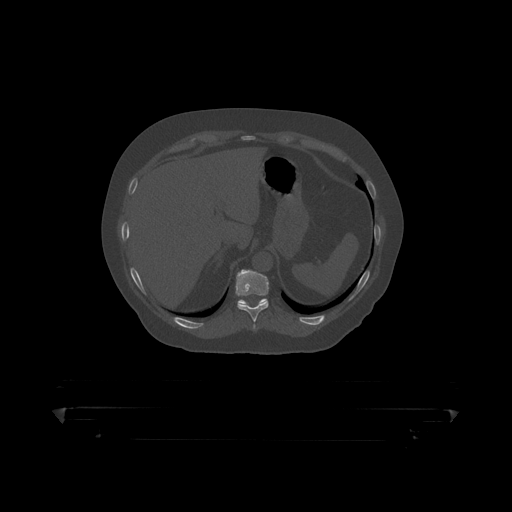
CT including the spine, one axial slice; slice 211 of 390 in the series (ordered by position); reconstruction kernel STANDARD; 120 kVp; bone window (W 1800 / L 400 HU); 1.25 mm slice thickness; 512 × 512 image matrix, field of view 650 × 650 mm. Male patient, age 60 years. From the clinical record (not read from this slice): primary cancer: prostate.
Outlined on this slice (semi-automatic segmentation, software-assisted and operator-edited):
- T10 vertebra: bounding box [x1, y1, x2, y2] px = [236, 270, 269, 319]
- T11 vertebra: [238, 298, 267, 305]